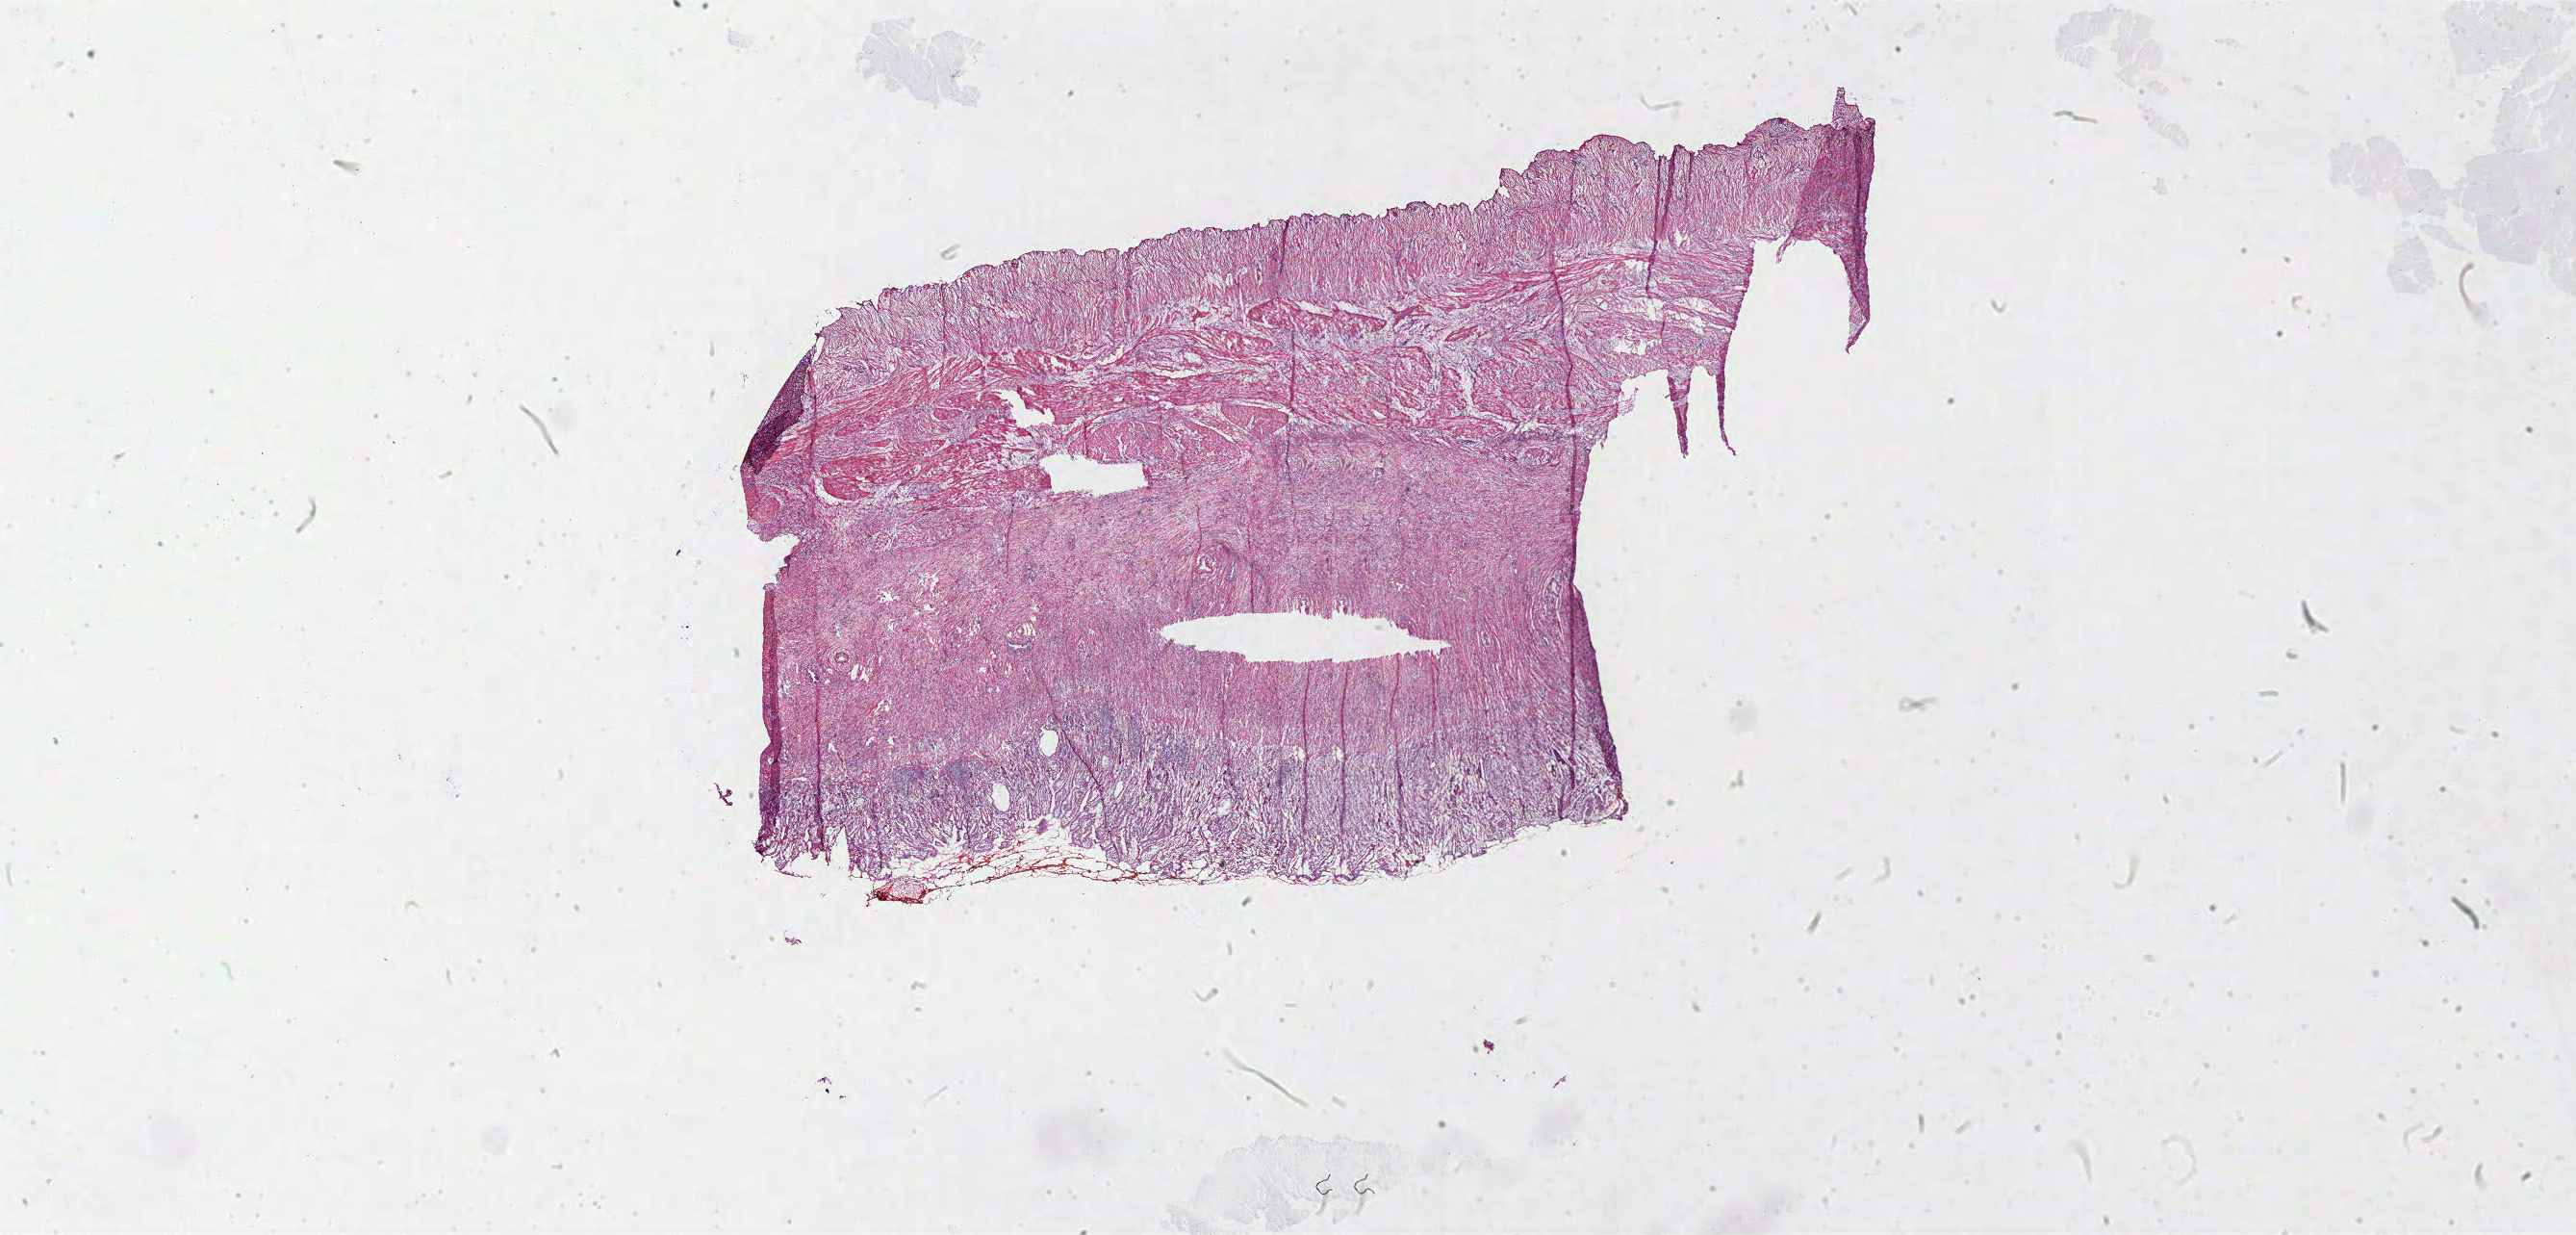
H&E-stained whole-slide image — shown as a low-resolution overview of the whole scanned area (about 42.2 x 20.2 mm, from a 40x scan), frozen section from the bottom of the tissue portion, primary tumour sample from the stomach. Patient: female, age at initial diagnosis 46 years. Histologic grade: G3 (poorly differentiated). Pathologist review of this section (percent, as recorded): tumour cells 65%, tumour nuclei 75%, normal cells 10%, stromal cells 25%, necrosis 0%.
Pathologic diagnosis: Adenocarcinoma, NOS (body of stomach). AJCC pathologic stage: IIIA. TNM: T3 N2 M0.